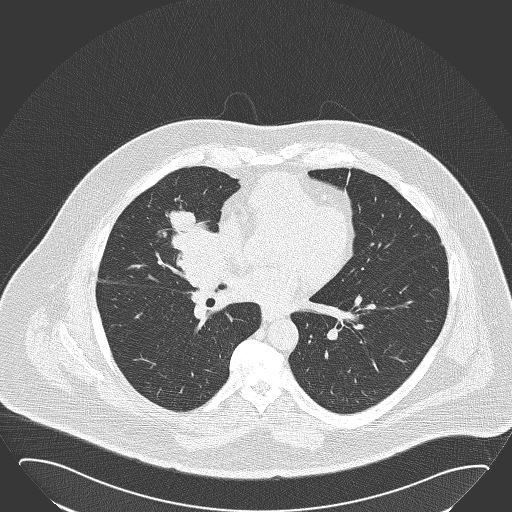
Chest CT (low-dose screening protocol), one axial image; baseline screening round; lung window (W 1500 / L -600 HU); 2 mm slice thickness; slice 92 of 168 in the series; 512 × 512 image matrix. Male, age 61 years at enrolment. Former smoker at enrolment.
- Lesion marked by an expert reader, bounding box <144,199,230,285> (left, top, right, bottom; pixels).
- The screening reader recorded 2 non-calcified nodules or masses ≥4 mm on this exam (right middle lobe, left lower lobe); which of them this box marks is not recorded.
- Official screen result: positive, change unspecified: nodule(s) >= 4 mm or enlarging nodule(s), mass(es), or other non-specific abnormalities suspicious for lung cancer.
- Lung cancer was diagnosed 47 days after this screen: basaloid squamous cell carcinoma, right middle lobe, right hilum, poorly differentiated (G3), stage IIB (AJCC 6th edition), 95 mm at pathology.